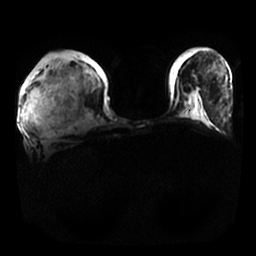
Breast MRI, one axial slice; position 4 of 25 along the scan axis; diffusion-weighted series; image 2 of 4 stored at this slice position (different b-values; order by instance number); 1.5 T; 4 mm slice thickness; 256 × 256 image matrix, field of view 350 × 350 mm. Female patient.
Outlined on this slice (expert manual segmentation):
- tumour on diffusion-weighted imaging: bounding box <28,82,47,124> (left, top, right, bottom; pixels)